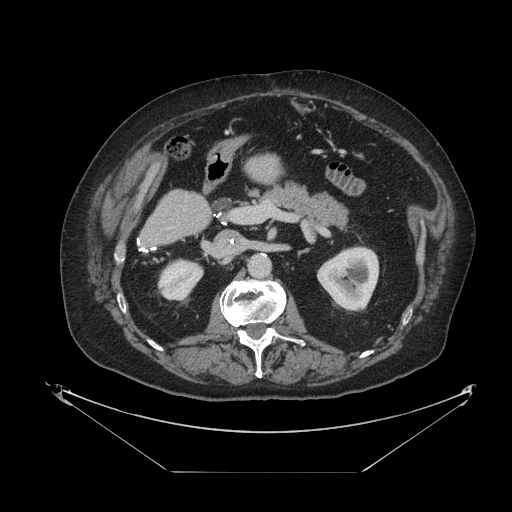
Contrast-enhanced abdominal CT, one axial slice. Position 42 of 121 along the scan axis. 120 kVp. Intravenous contrast given. Soft-tissue window (W 400 / L 40 HU). 2.5 mm slice thickness. 512 × 512 image matrix. Male patient, age 68 years. From the clinical record (not read from this slice): diagnosis: colorectal cancer liver metastases, imaged before liver resection; multiple liver metastases: no; largest metastasis: 4 cm; chemotherapy before resection: yes.
Annotated regions visible in this slice (outlined manually by an expert reader):
- liver: bounding box (x1, y1, x2, y2) in pixels: (142, 155, 282, 246)
- planned liver remnant (the part of the liver to remain after resection): (142, 154, 282, 246)